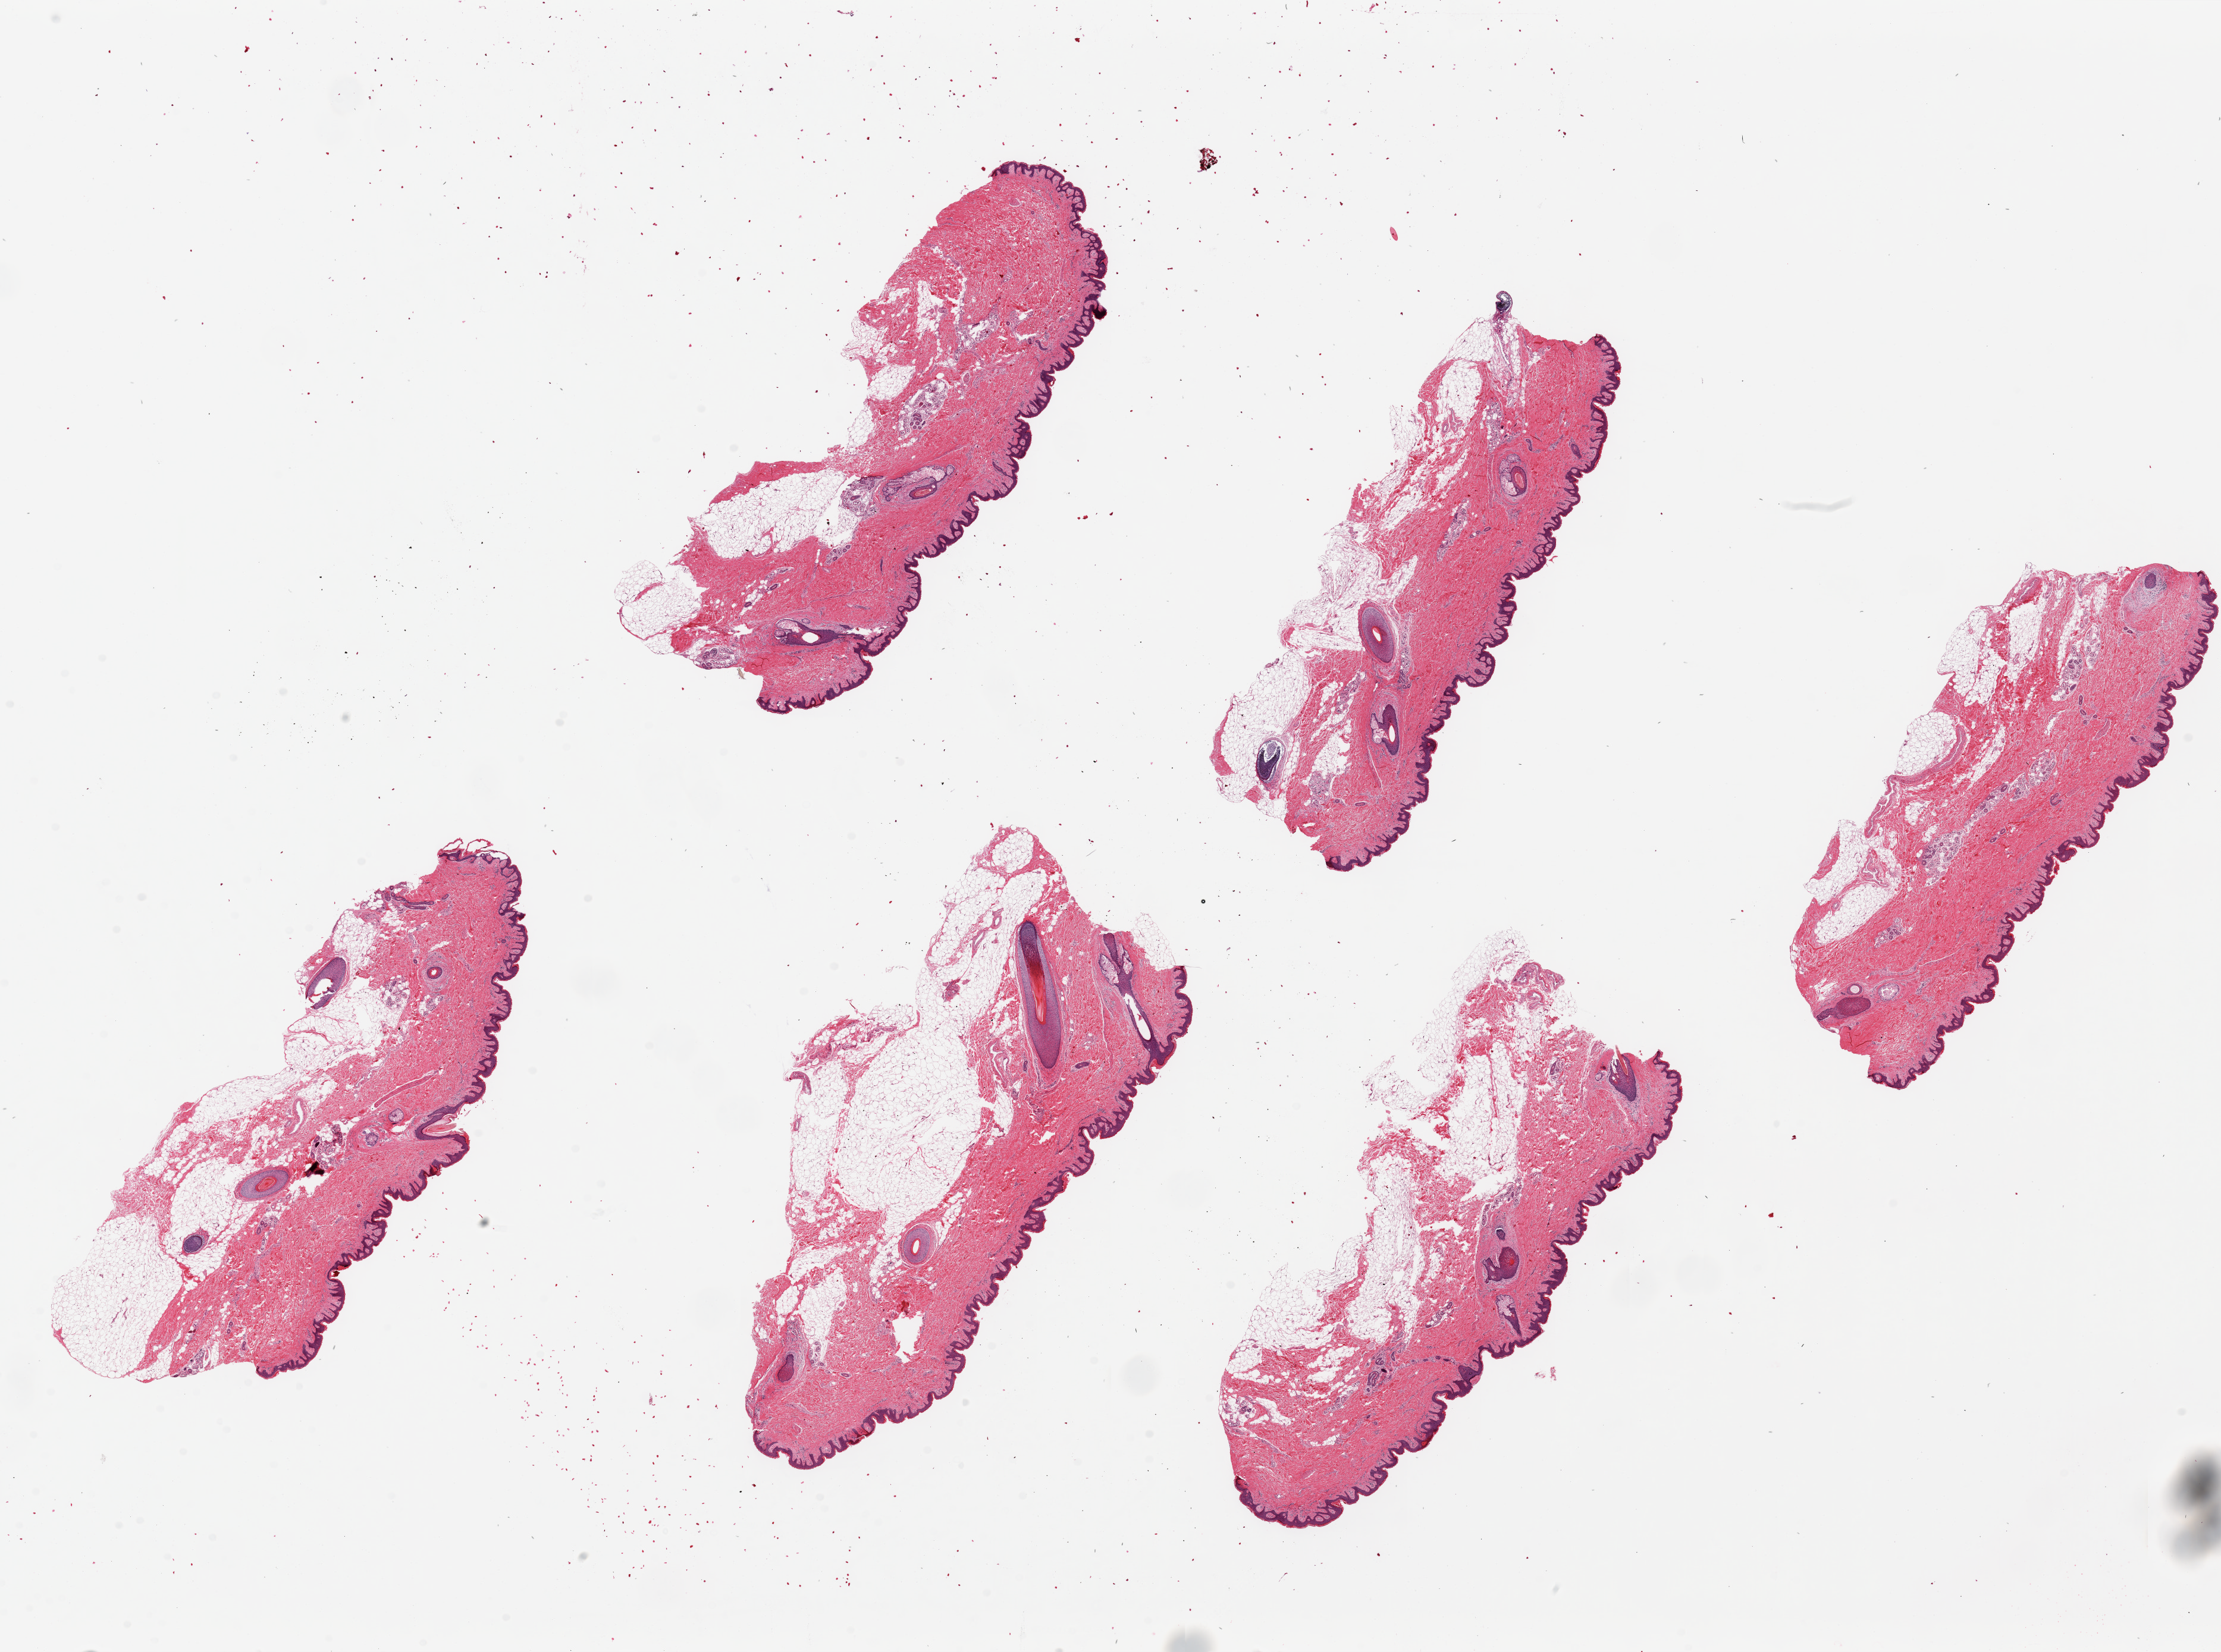
Digitized H&E-stained section, whole scanned area (about 29.5 x 22.0 mm, acquisition: 20x scan) shown as a low-resolution overview, PAXgene-fixed paraffin-embedded (PFPE) section, sampled site (target tissue): skin of suprapubic region, donor tissue sample. Donor sex: male.
* reviewer comment on this tissue sample: 6 pieces ~7x3mm